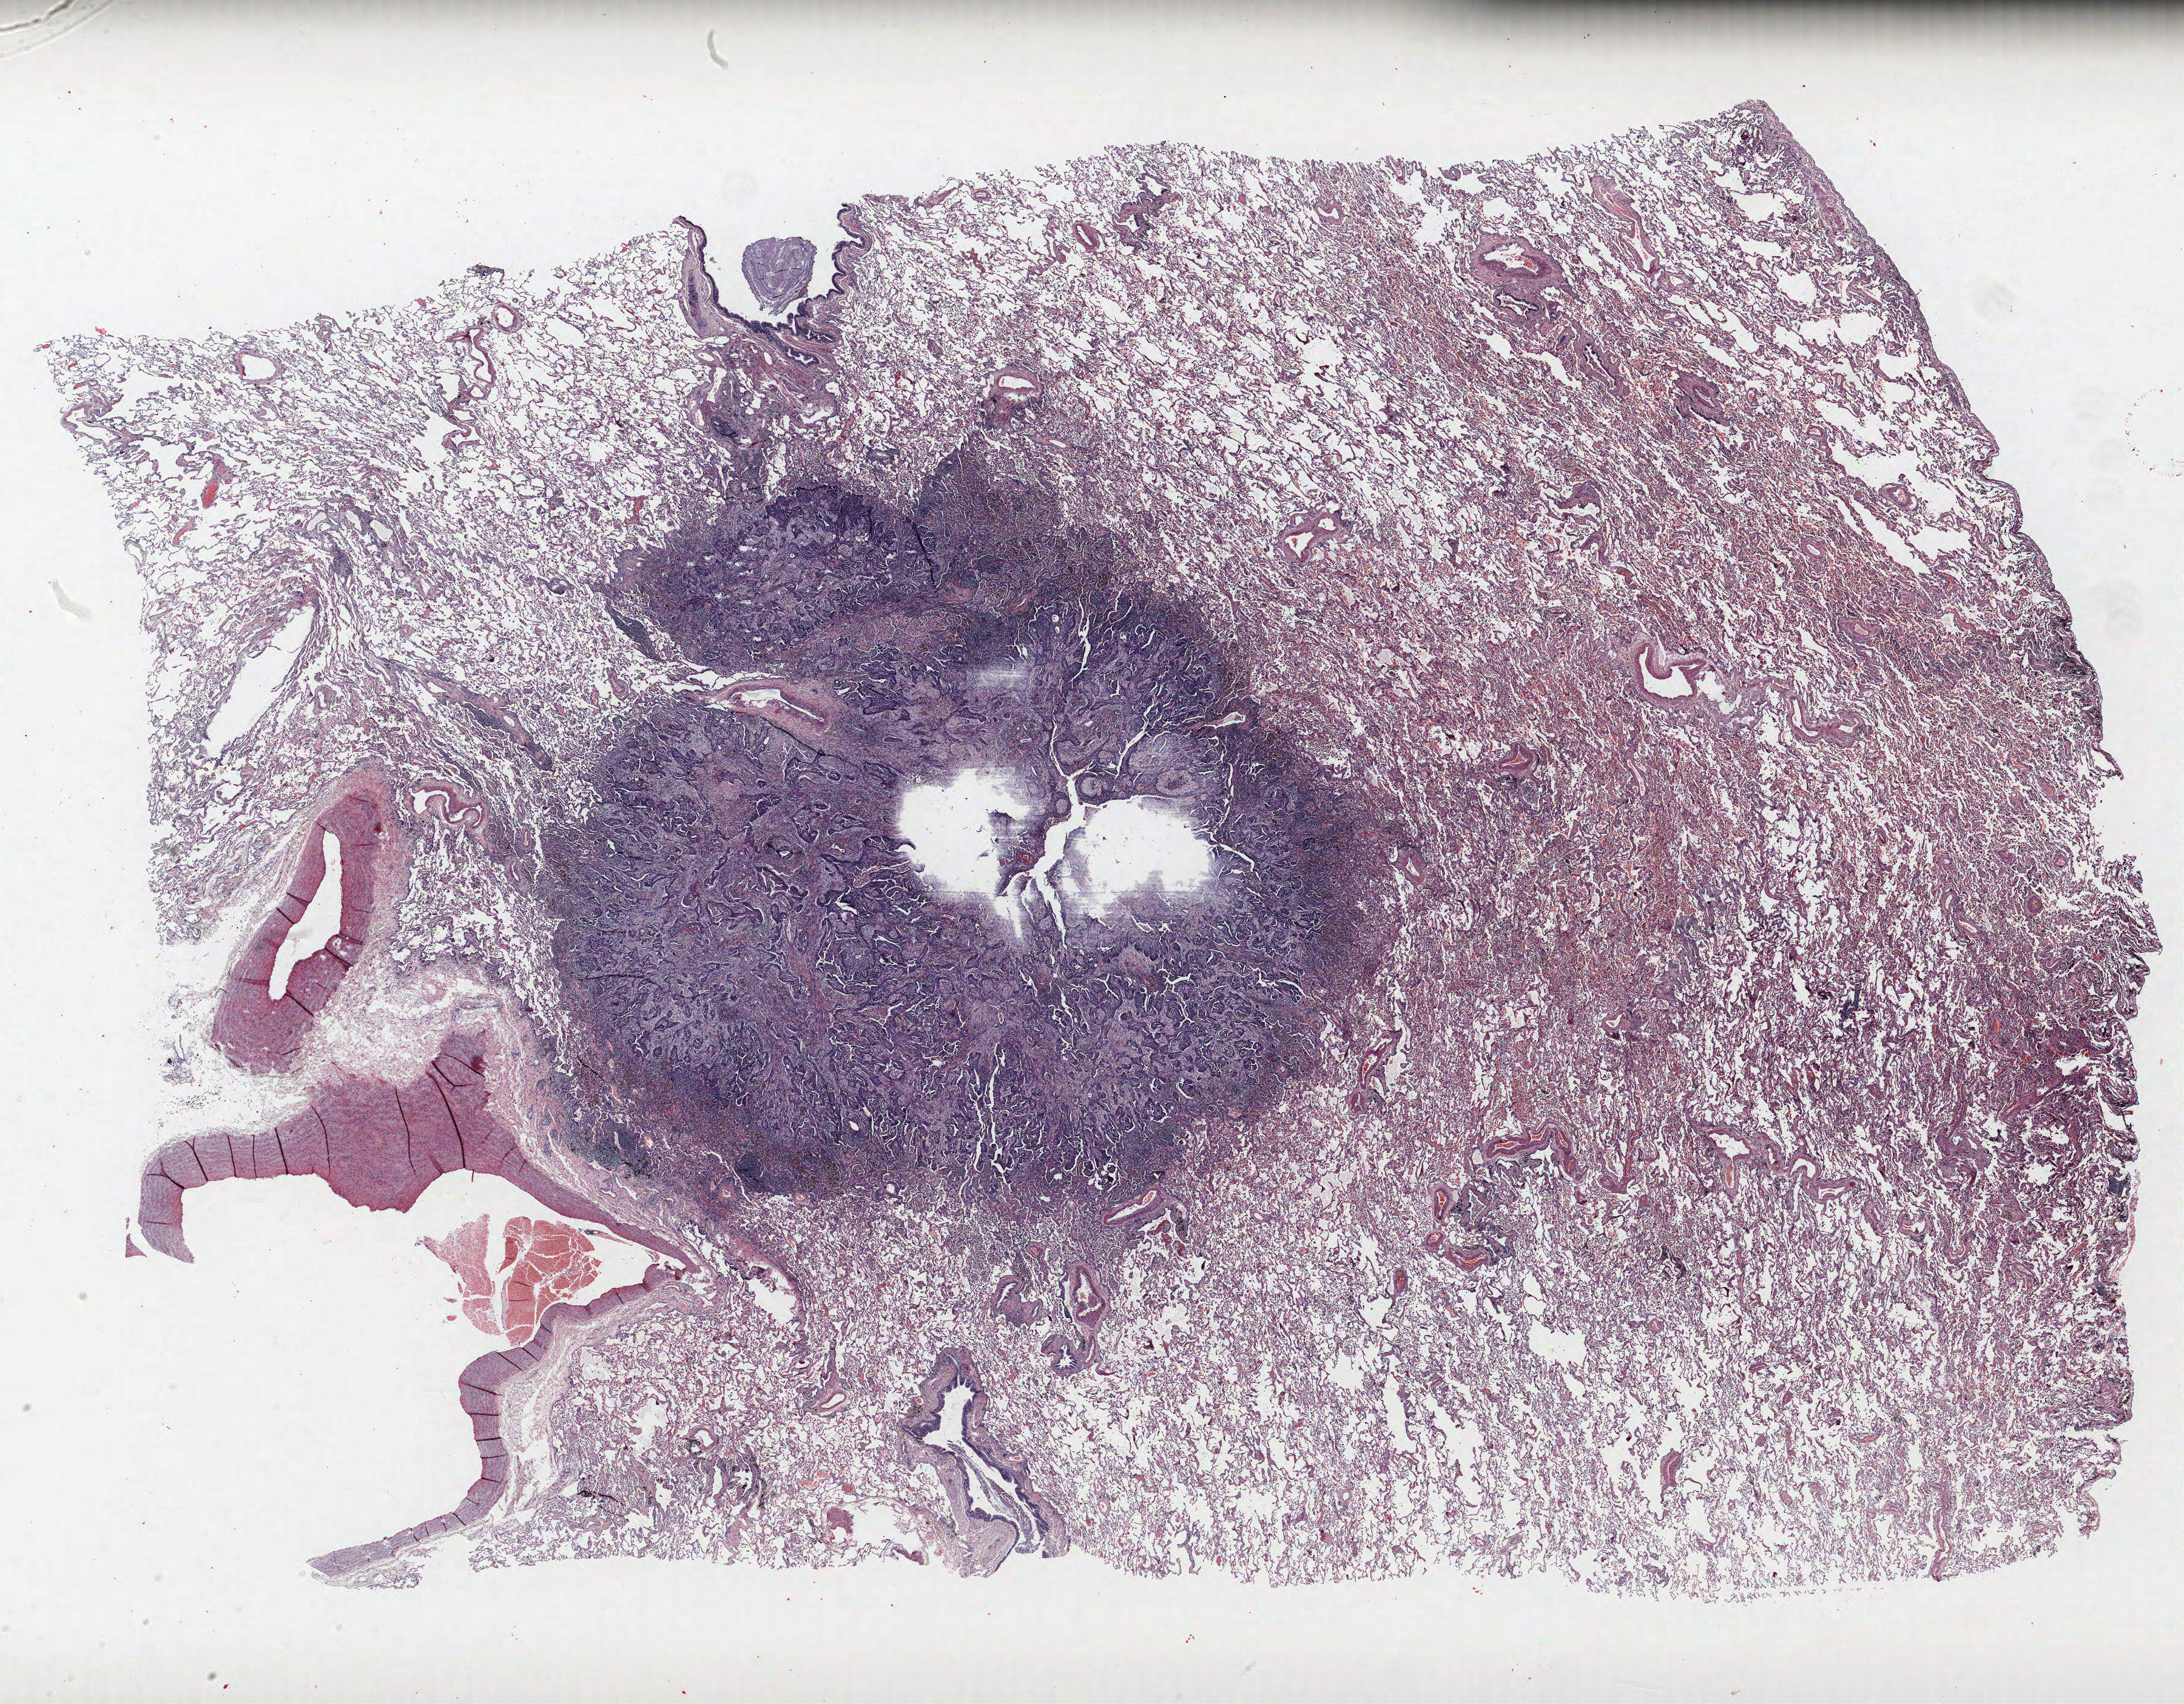
H&E-stained whole-slide image, low-resolution overview of the scanned area, about 28.8 x 22.5 mm, formalin-fixed paraffin-embedded (FFPE) section, lung. Male, age 62 at enrolment. Former smoker at enrolment. Grade: well differentiated (G1).
Primary tumour location (clinical record): left upper lobe. Tumour size (pathology): 15 mm. Participant's lung-cancer diagnosis: Squamous cell carcinoma, NOS. Stage (AJCC 6th edition): IA. Note: participant had 2 primary lung cancers recorded; fields above describe the first.